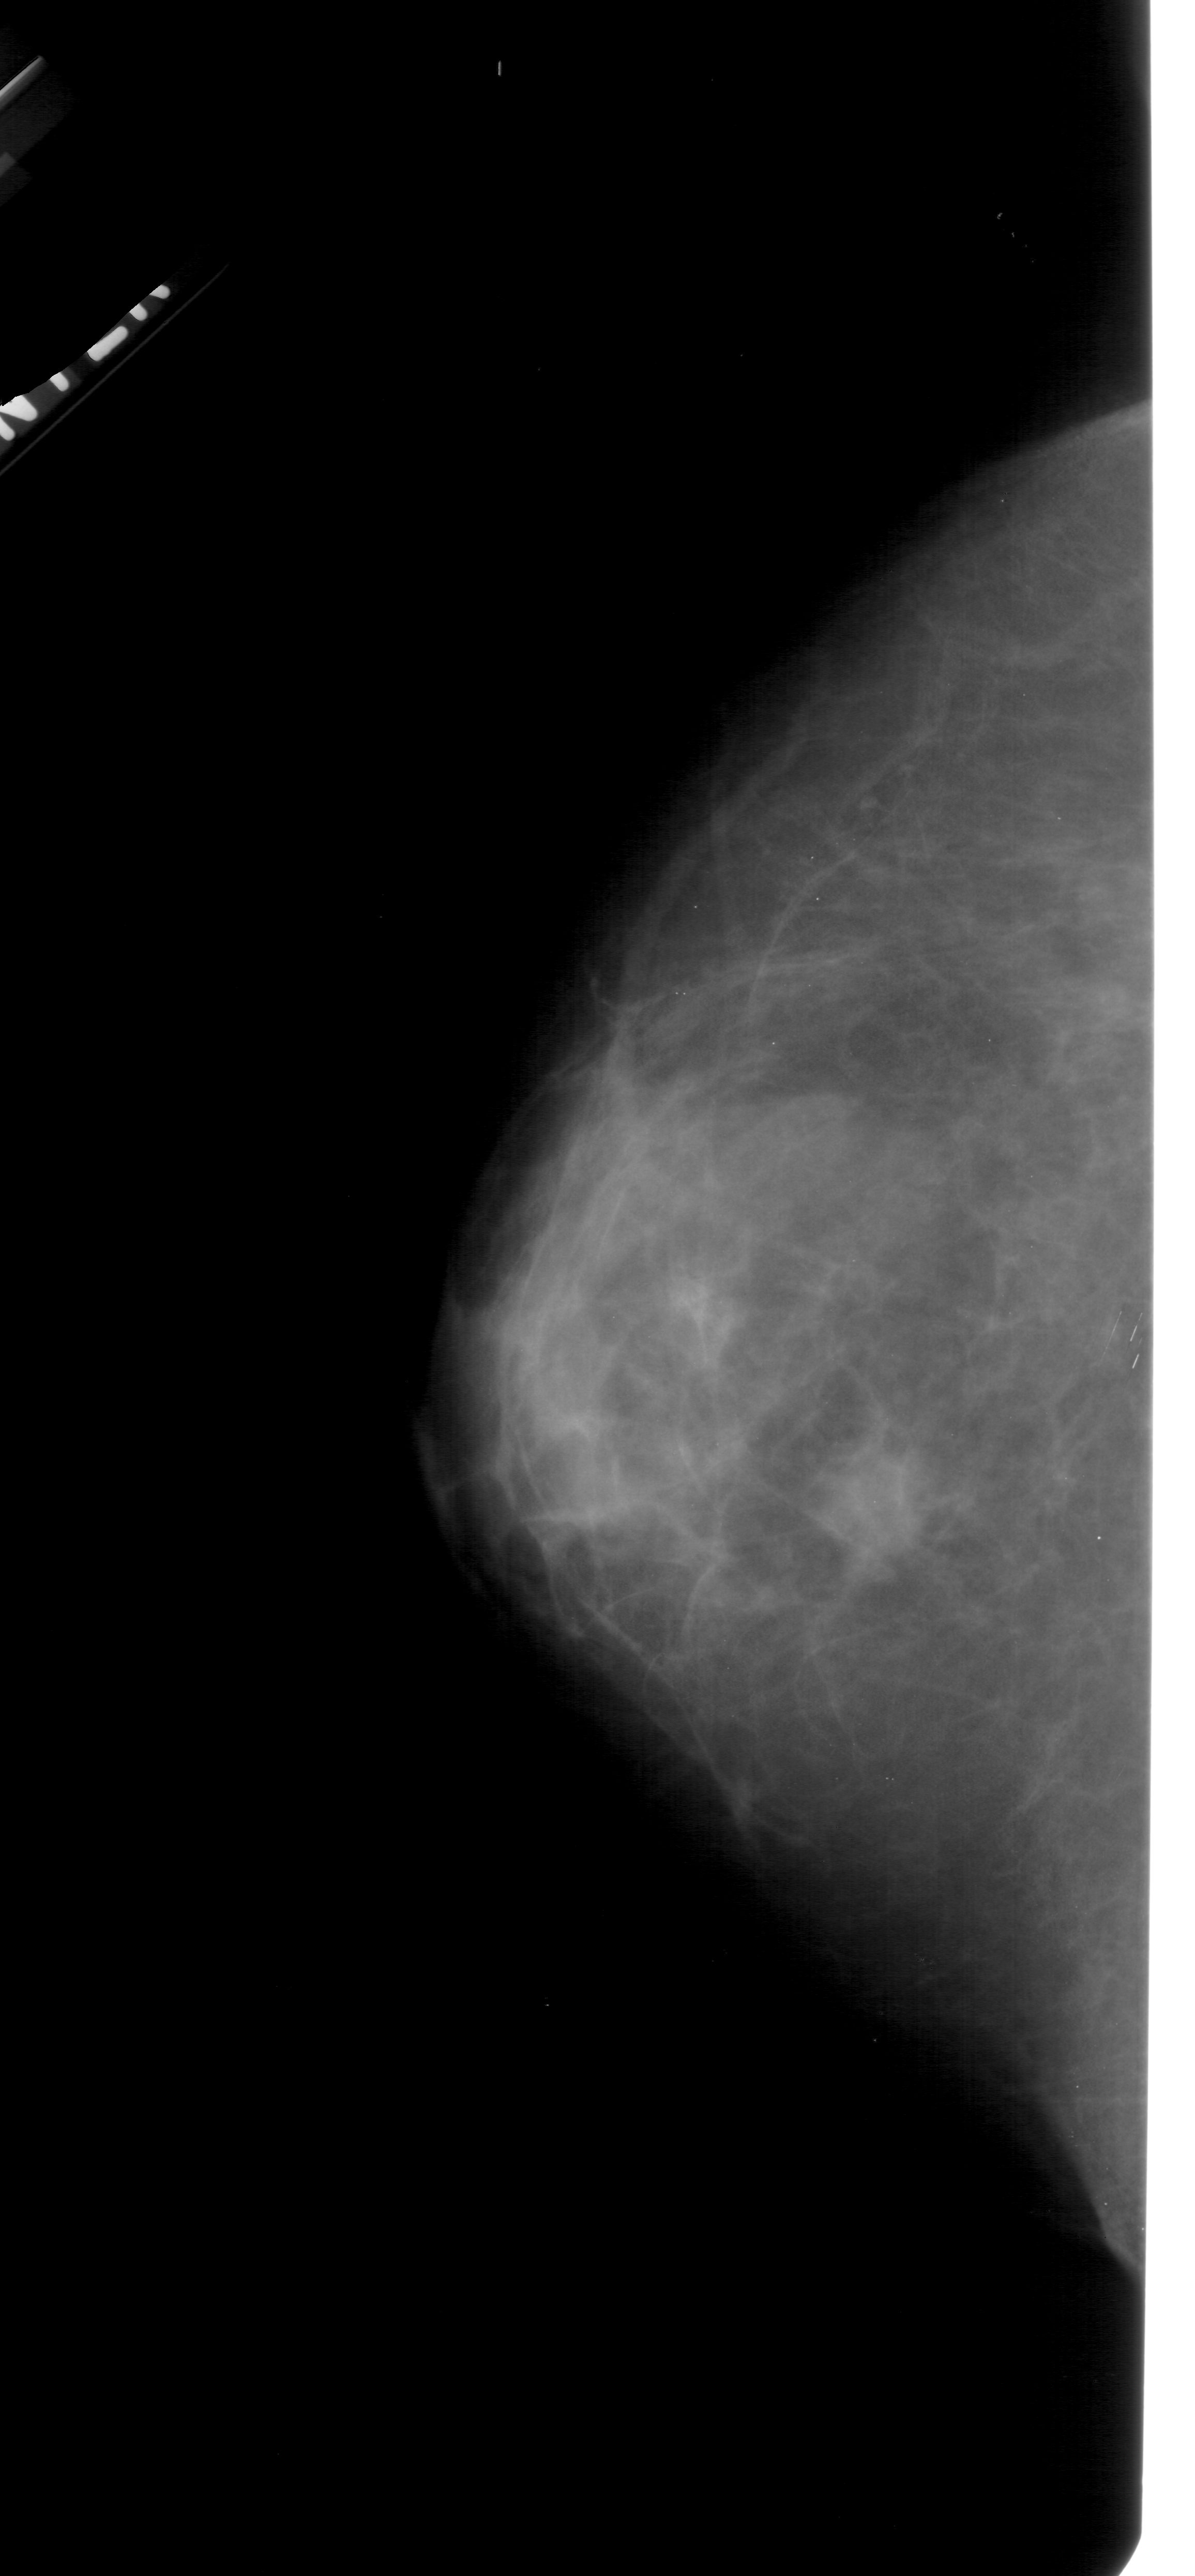
Digitized screen-film mammogram. Left breast. CC view. 1195 × 2576 image matrix.
Marked abnormalities (boxes around the expert regions of interest):
- mass, shape irregular, margins ill defined; BI-RADS assessment category 4; pathology result (as recorded, not read from the image): malignant: box from (x=636, y=1250) to (x=762, y=1388) px